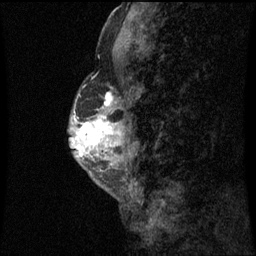
Breast MRI (dynamic contrast-enhanced), one sagittal slice; dynamic contrast-enhanced series, image 2 of 3 at this slice position (ordered by acquisition); 1.5 T; TE 4.2 ms, TR 8.9 ms; 2 mm slice thickness; 256 × 256 image matrix, field of view 200 × 200 mm. Female patient, age 50 years. From the clinical record (not read from this slice): setting: breast cancer imaged before/during neoadjuvant chemotherapy; receptor status: triple-negative.
Annotated regions visible in this slice (semi-automatic segmentation, software-assisted and operator-edited):
- analysis volume of interest (the breast-tissue region the enhancement analysis was run in; not a lesion): bounding box [x1, y1, x2, y2] px = [70, 82, 116, 169]
- tumour enhancement mask (voxels above the 70 % enhancement threshold inside the analysis volume of interest): [74, 92, 114, 149]